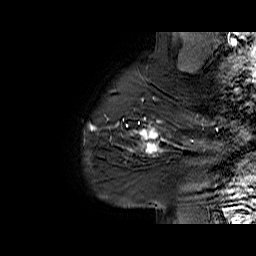
Breast MRI (dynamic contrast-enhanced), one sagittal slice; position 54 of 60 along the scan axis; dynamic contrast-enhanced series, time point 2 of 6 at this slice position (early post-contrast); 1.5 T; TE 6.1 ms, TR 32.9 ms; 4 mm slice thickness; 256 × 256 image matrix, field of view 220 × 220 mm. Female patient. Case-level facts recorded for this patient, not image findings: setting: breast cancer imaged before/during neoadjuvant chemotherapy; receptor status: HER2-positive.
Outlined on this slice (semi-automatically segmented with operator editing):
- analysis volume of interest (the breast-tissue region the enhancement analysis was run in; not a lesion): bounding box [x1, y1, x2, y2] px = [127, 95, 194, 165]
- tumour enhancement mask (voxels above the 100 % enhancement threshold inside the analysis volume of interest): [127, 98, 194, 152]